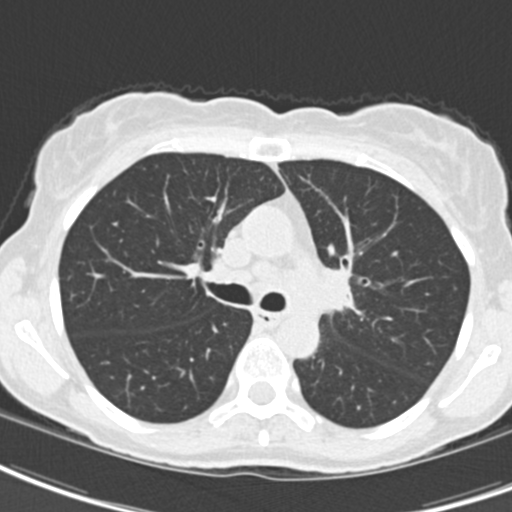
Chest CT (low-dose screening protocol), one axial image. Baseline annual screen. Lung window (W 1500 / L -600 HU). Slice 61 of 189 in the series. 512 × 512 image matrix. Female, age 62 years at enrolment. Current smoker at enrolment.
Expert-annotated lung lesion, box from (x=294, y=250) to (x=368, y=334) px. The exam's reader record, not a measurement of the box and not confirmed to be the same lesion: non-calcified nodule or mass ≥4 mm, right upper lobe, 24 × 20 mm, smooth margins, ground glass attenuation. Note: the box lies in the patient's left hemithorax on this image, whereas the reader's record names the right lung; they may be different findings. Official screen result: positive, change unspecified: nodule(s) >= 4 mm or enlarging nodule(s), mass(es), or other non-specific abnormalities suspicious for lung cancer. Lung cancer was diagnosed 24 days after this screen: oat cell carcinoma, left hilum, left main stem bronchus, stage IIIB (AJCC 6th edition), 50 mm at pathology.